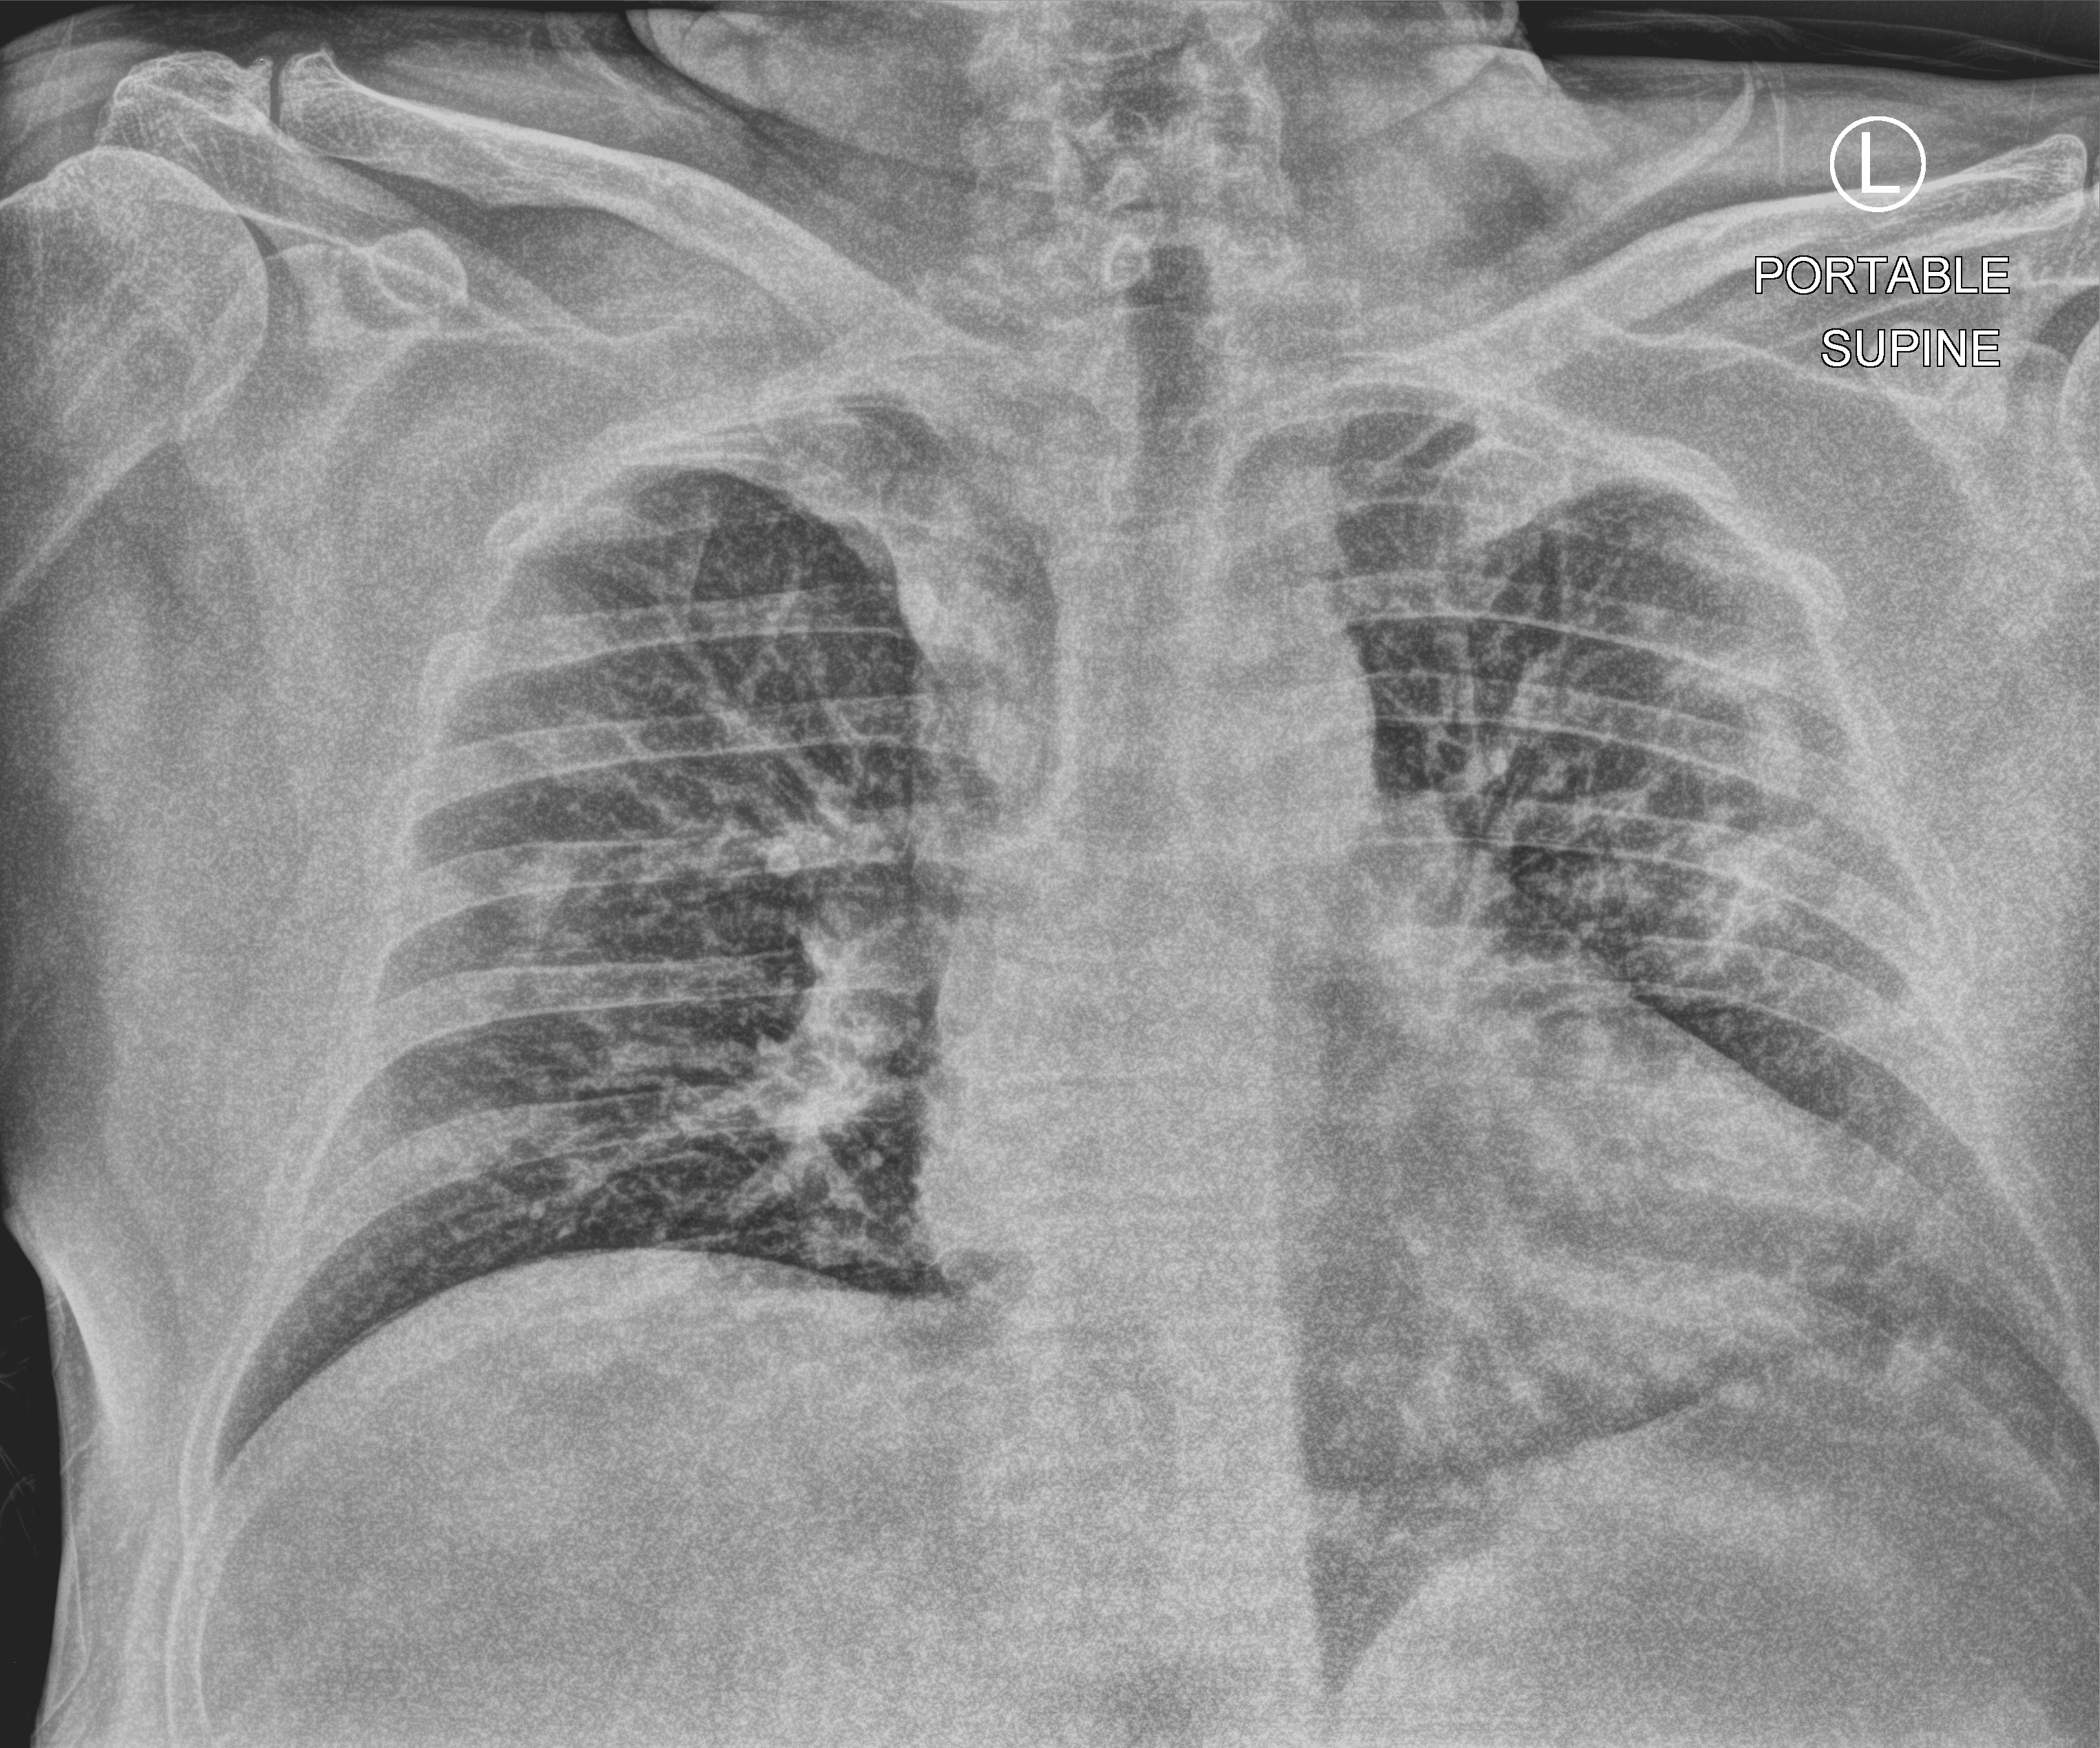
Bedside chest radiograph (computed radiography); anteroposterior (AP) projection. Male patient hospitalised with COVID-19, age 60–74 years.
Hospital-stay facts (about this admission, not read from this image; timing relative to this image not recorded):
- COPD (admission record): no
- hypertension (admission record): no
- chronic kidney disease (admission record): no